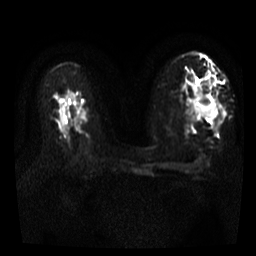
Breast MRI, one axial slice. Position 17 of 35 along the scan axis. Diffusion-weighted series; image 2 of 4 stored at this slice position (different b-values; order by instance number). 3 T. 5 mm slice thickness. 256 × 256 image matrix, field of view 300 × 300 mm. Female patient.
Annotated regions visible in this slice (manually delineated by an expert):
- tumour on diffusion-weighted imaging: bounding box [x1, y1, x2, y2] px = [192, 104, 217, 118]